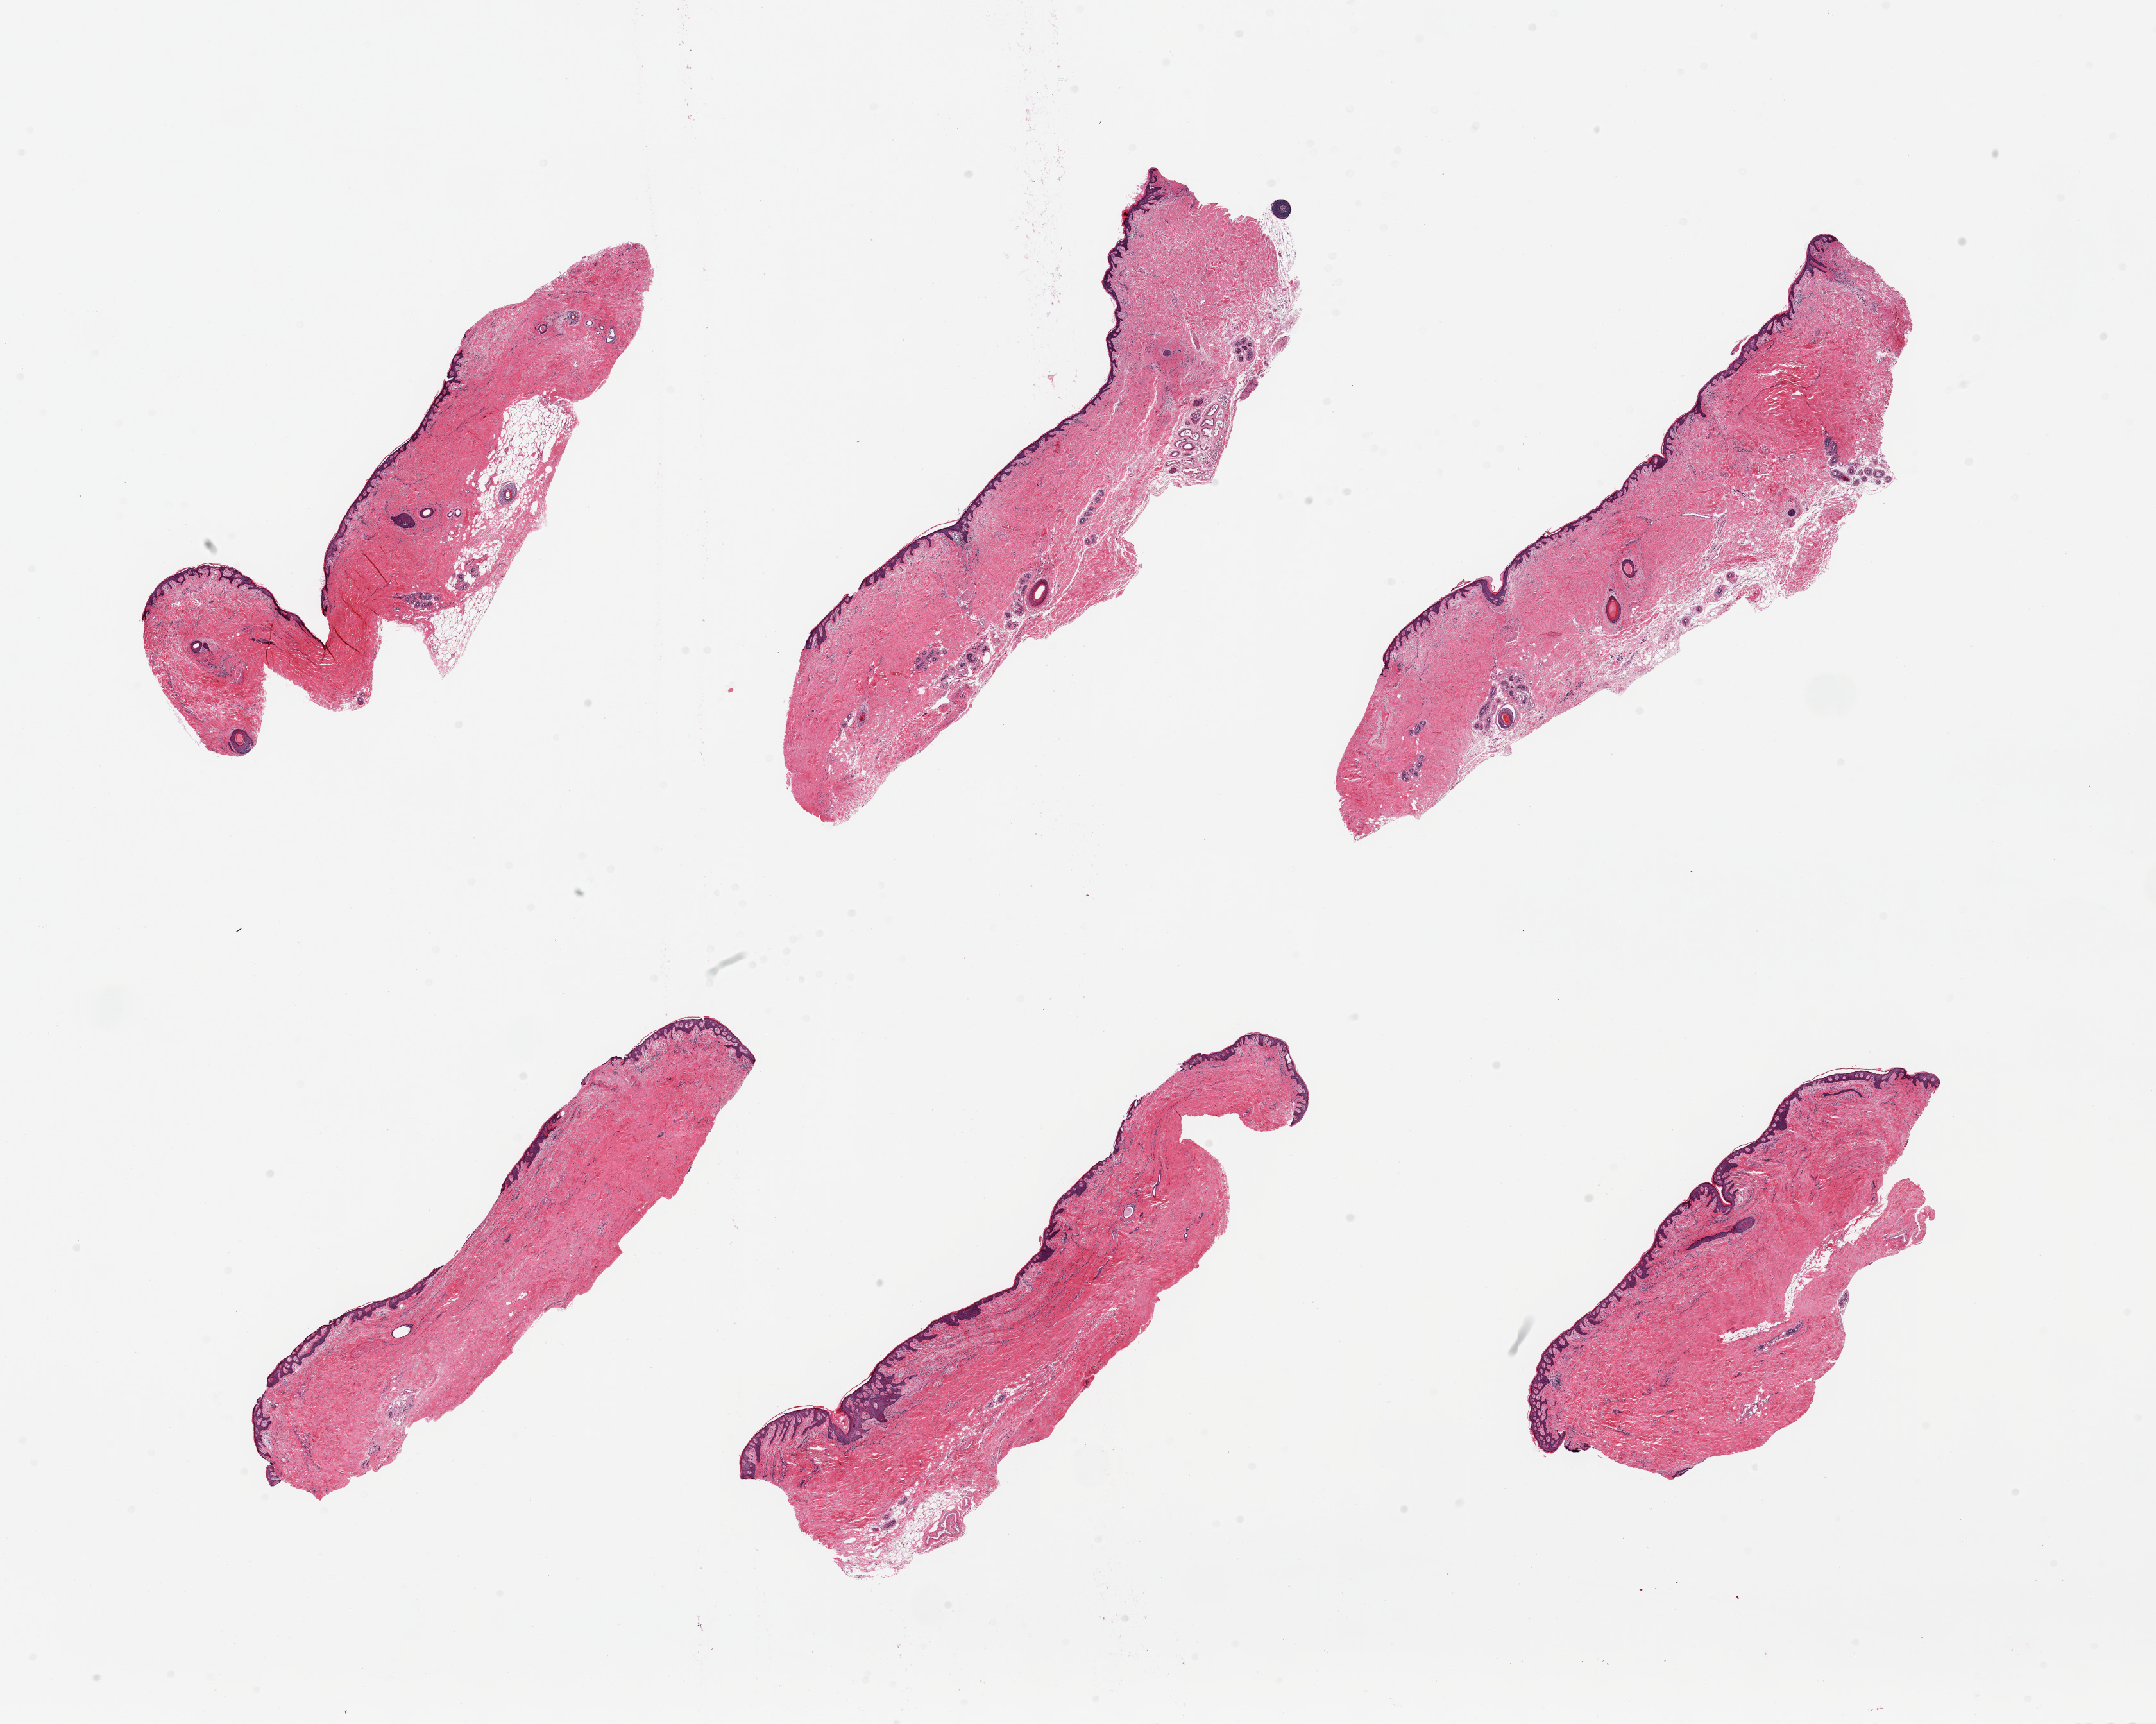
Hematoxylin and eosin (H&E) whole-slide image, brightfield, low-resolution overview of the scanned area, about 26.6 x 21.2 mm, PAXgene-fixed paraffin-embedded (PFPE) section, section of skin of suprapubic region (target tissue), donor tissue sample. Donor: female.
Reviewer comment on this tissue sample: 6 pieces, minimal fat, squamous epithelium is ~ 50microns.